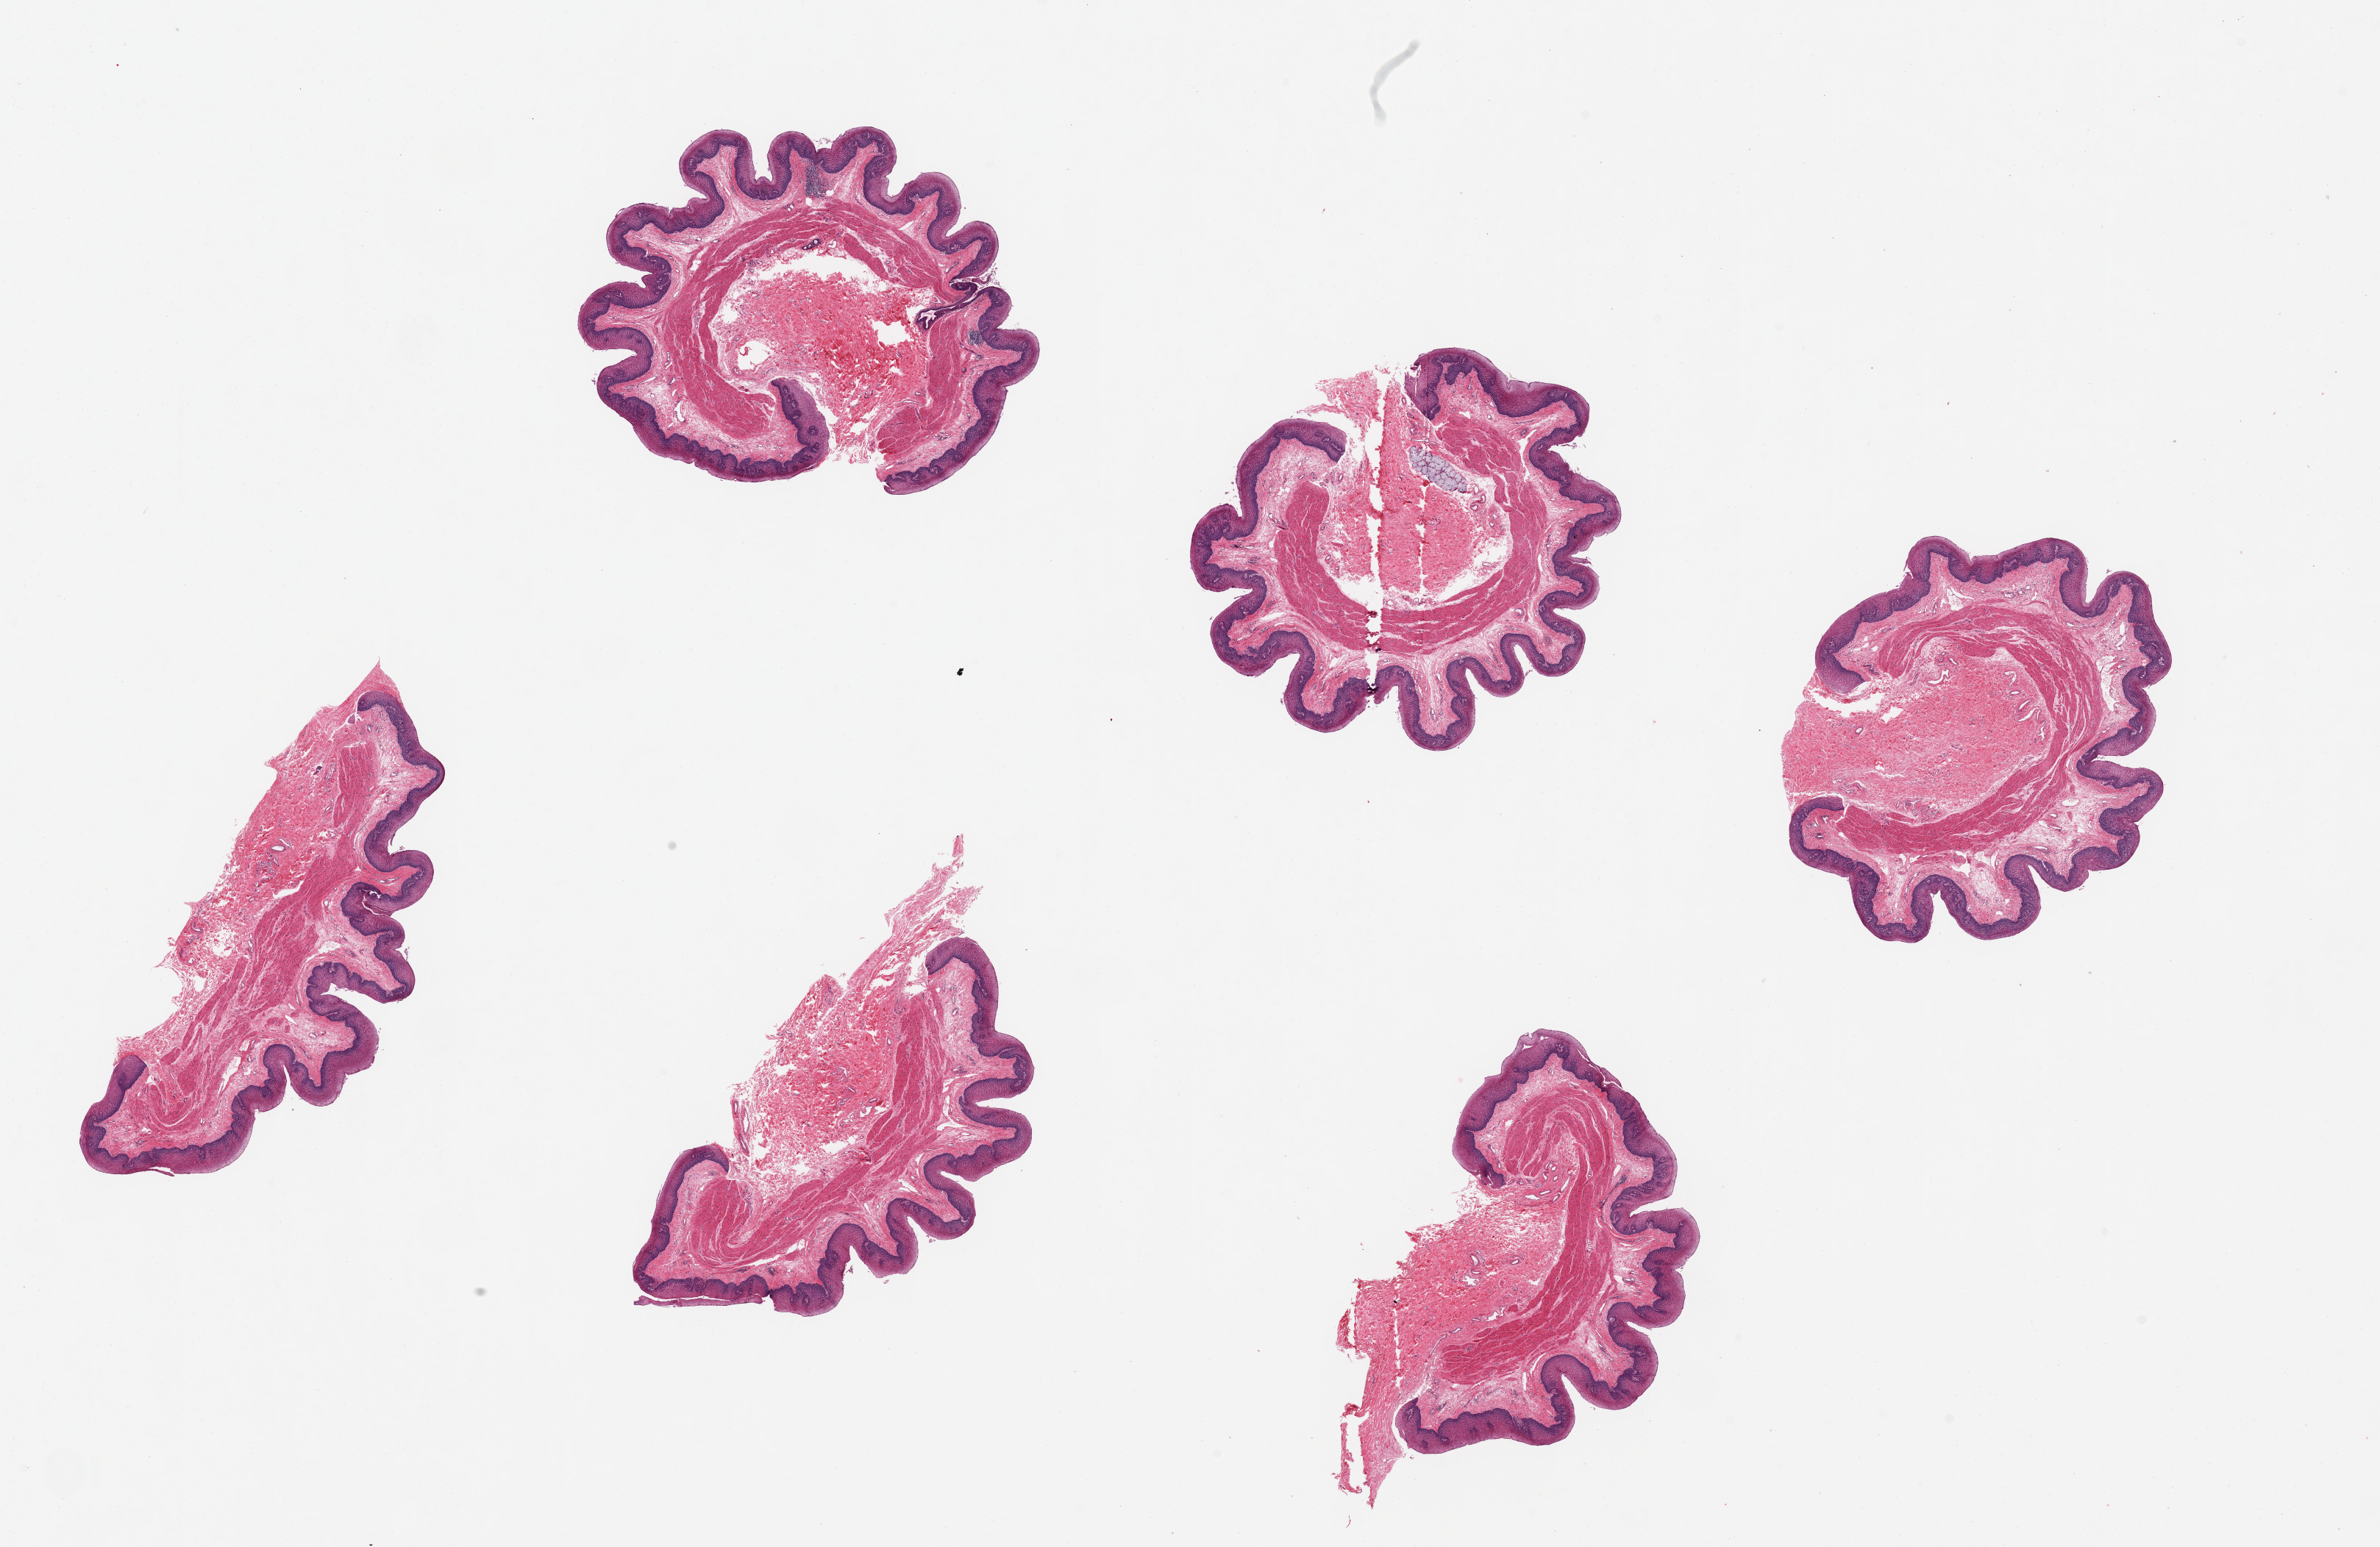
Hematoxylin and eosin (H&E) whole-slide image, shown as a low-resolution overview of the whole scanned area (about 25.6 x 16.6 mm), PAXgene-fixed paraffin-embedded (PFPE) section, section of esophageal mucous membrane (target tissue), tissue donor sample. Donor: female.
Review note (as recorded): 6 pieces up to 6x4 mm; excellent specimen.